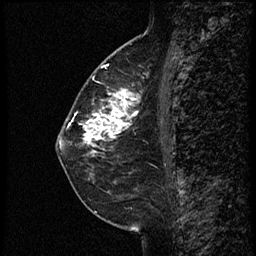
Breast MRI (dynamic contrast-enhanced), one sagittal slice. Dynamic contrast-enhanced study with each time point stored as its own series, time point 2 of 3 at this slice position (early post-contrast, ordered by acquisition time). 1.5 T. TE 4.2 ms, TR 18.9 ms. 256 × 256 image matrix, field of view 200 × 200 mm. Female patient. From the clinical record (not read from this slice): setting: breast cancer imaged before/during neoadjuvant chemotherapy; receptor status: HER2-positive.
Structures marked on this image (semi-automatically segmented with operator editing):
- analysis volume of interest (the breast-tissue region the enhancement analysis was run in; not a lesion): bounding box <77,66,148,147> (left, top, right, bottom; pixels)
- tumour enhancement mask (voxels above the 100 % enhancement threshold inside the analysis volume of interest): <84,85,142,147>